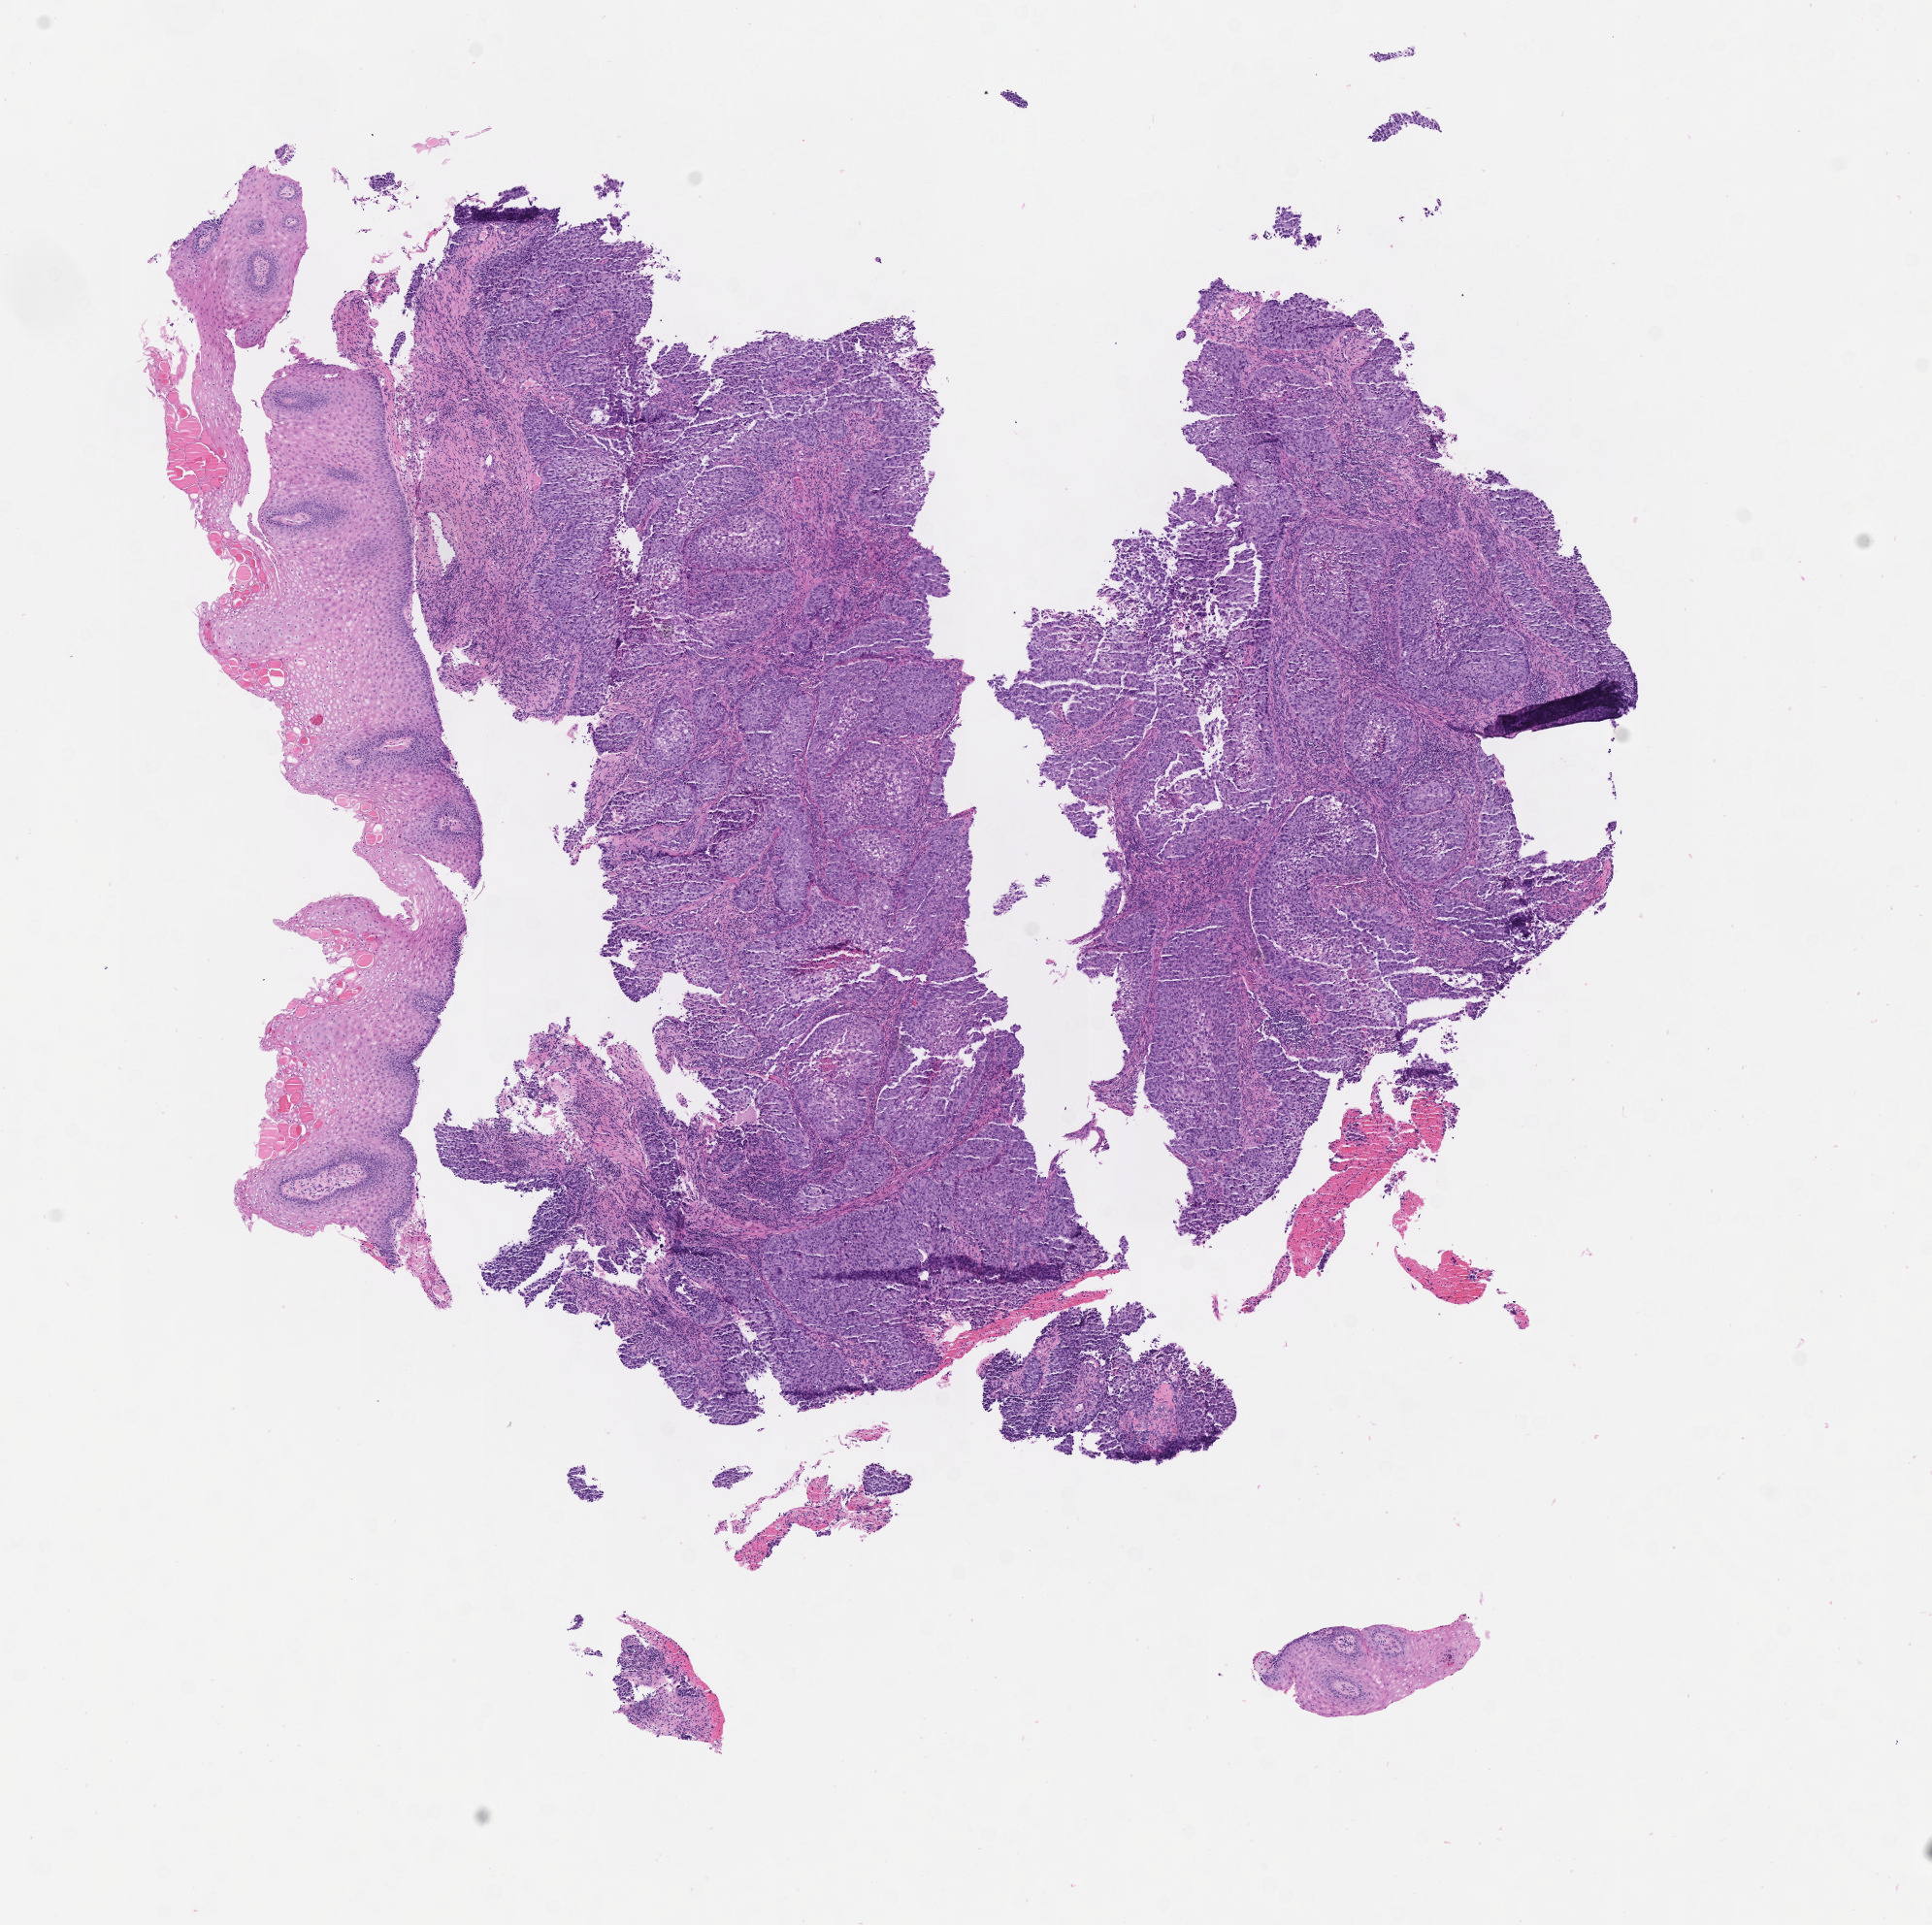
Whole-slide image, H&E stain, whole scanned area (about 8.1 x 8.0 mm) shown as a low-resolution overview. Tumor tissue. Anatomic site: cervix. Patient: female, 33 years old.
Diagnosis: Squamous cell carcinoma, large cell, nonkeratinizing, NOS.